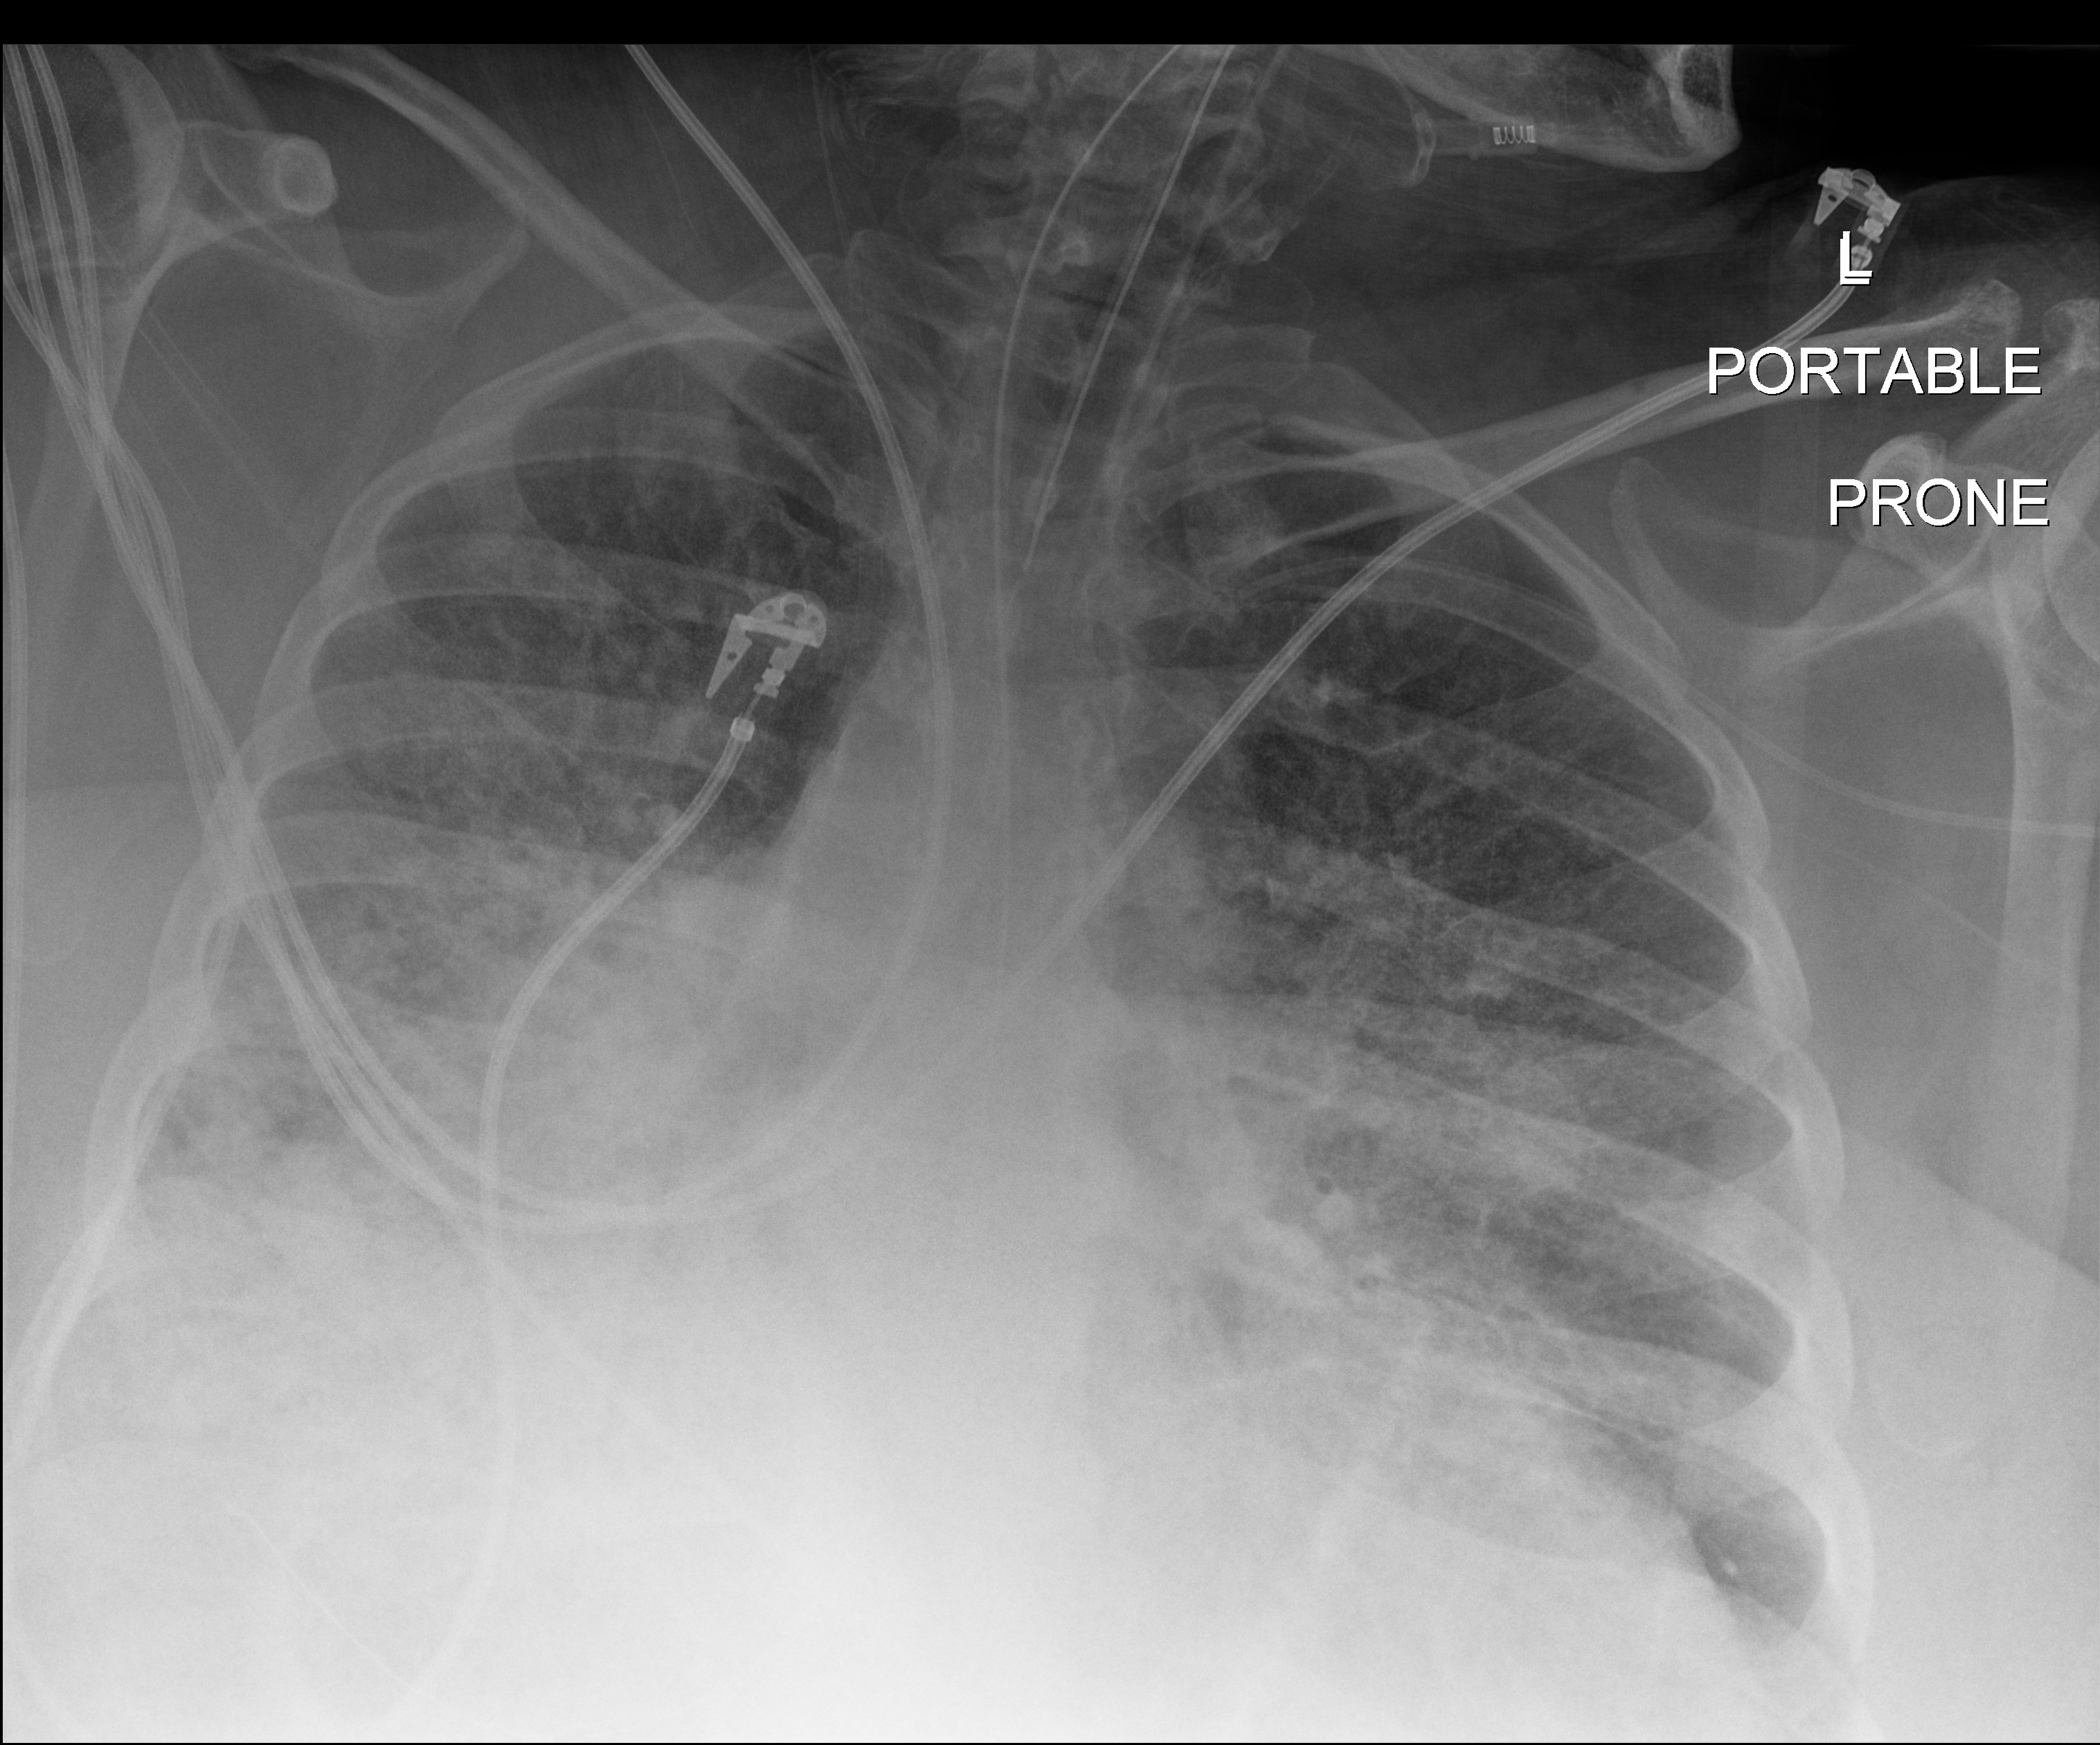
Chest radiograph (digital radiography), posteroanterior (PA) projection. Adult patient hospitalised with COVID-19, age 18–59 years.
Admission-level facts for this patient (not findings on this image; timing relative to this image not recorded): admitted to intensive care during this hospital stay: yes.